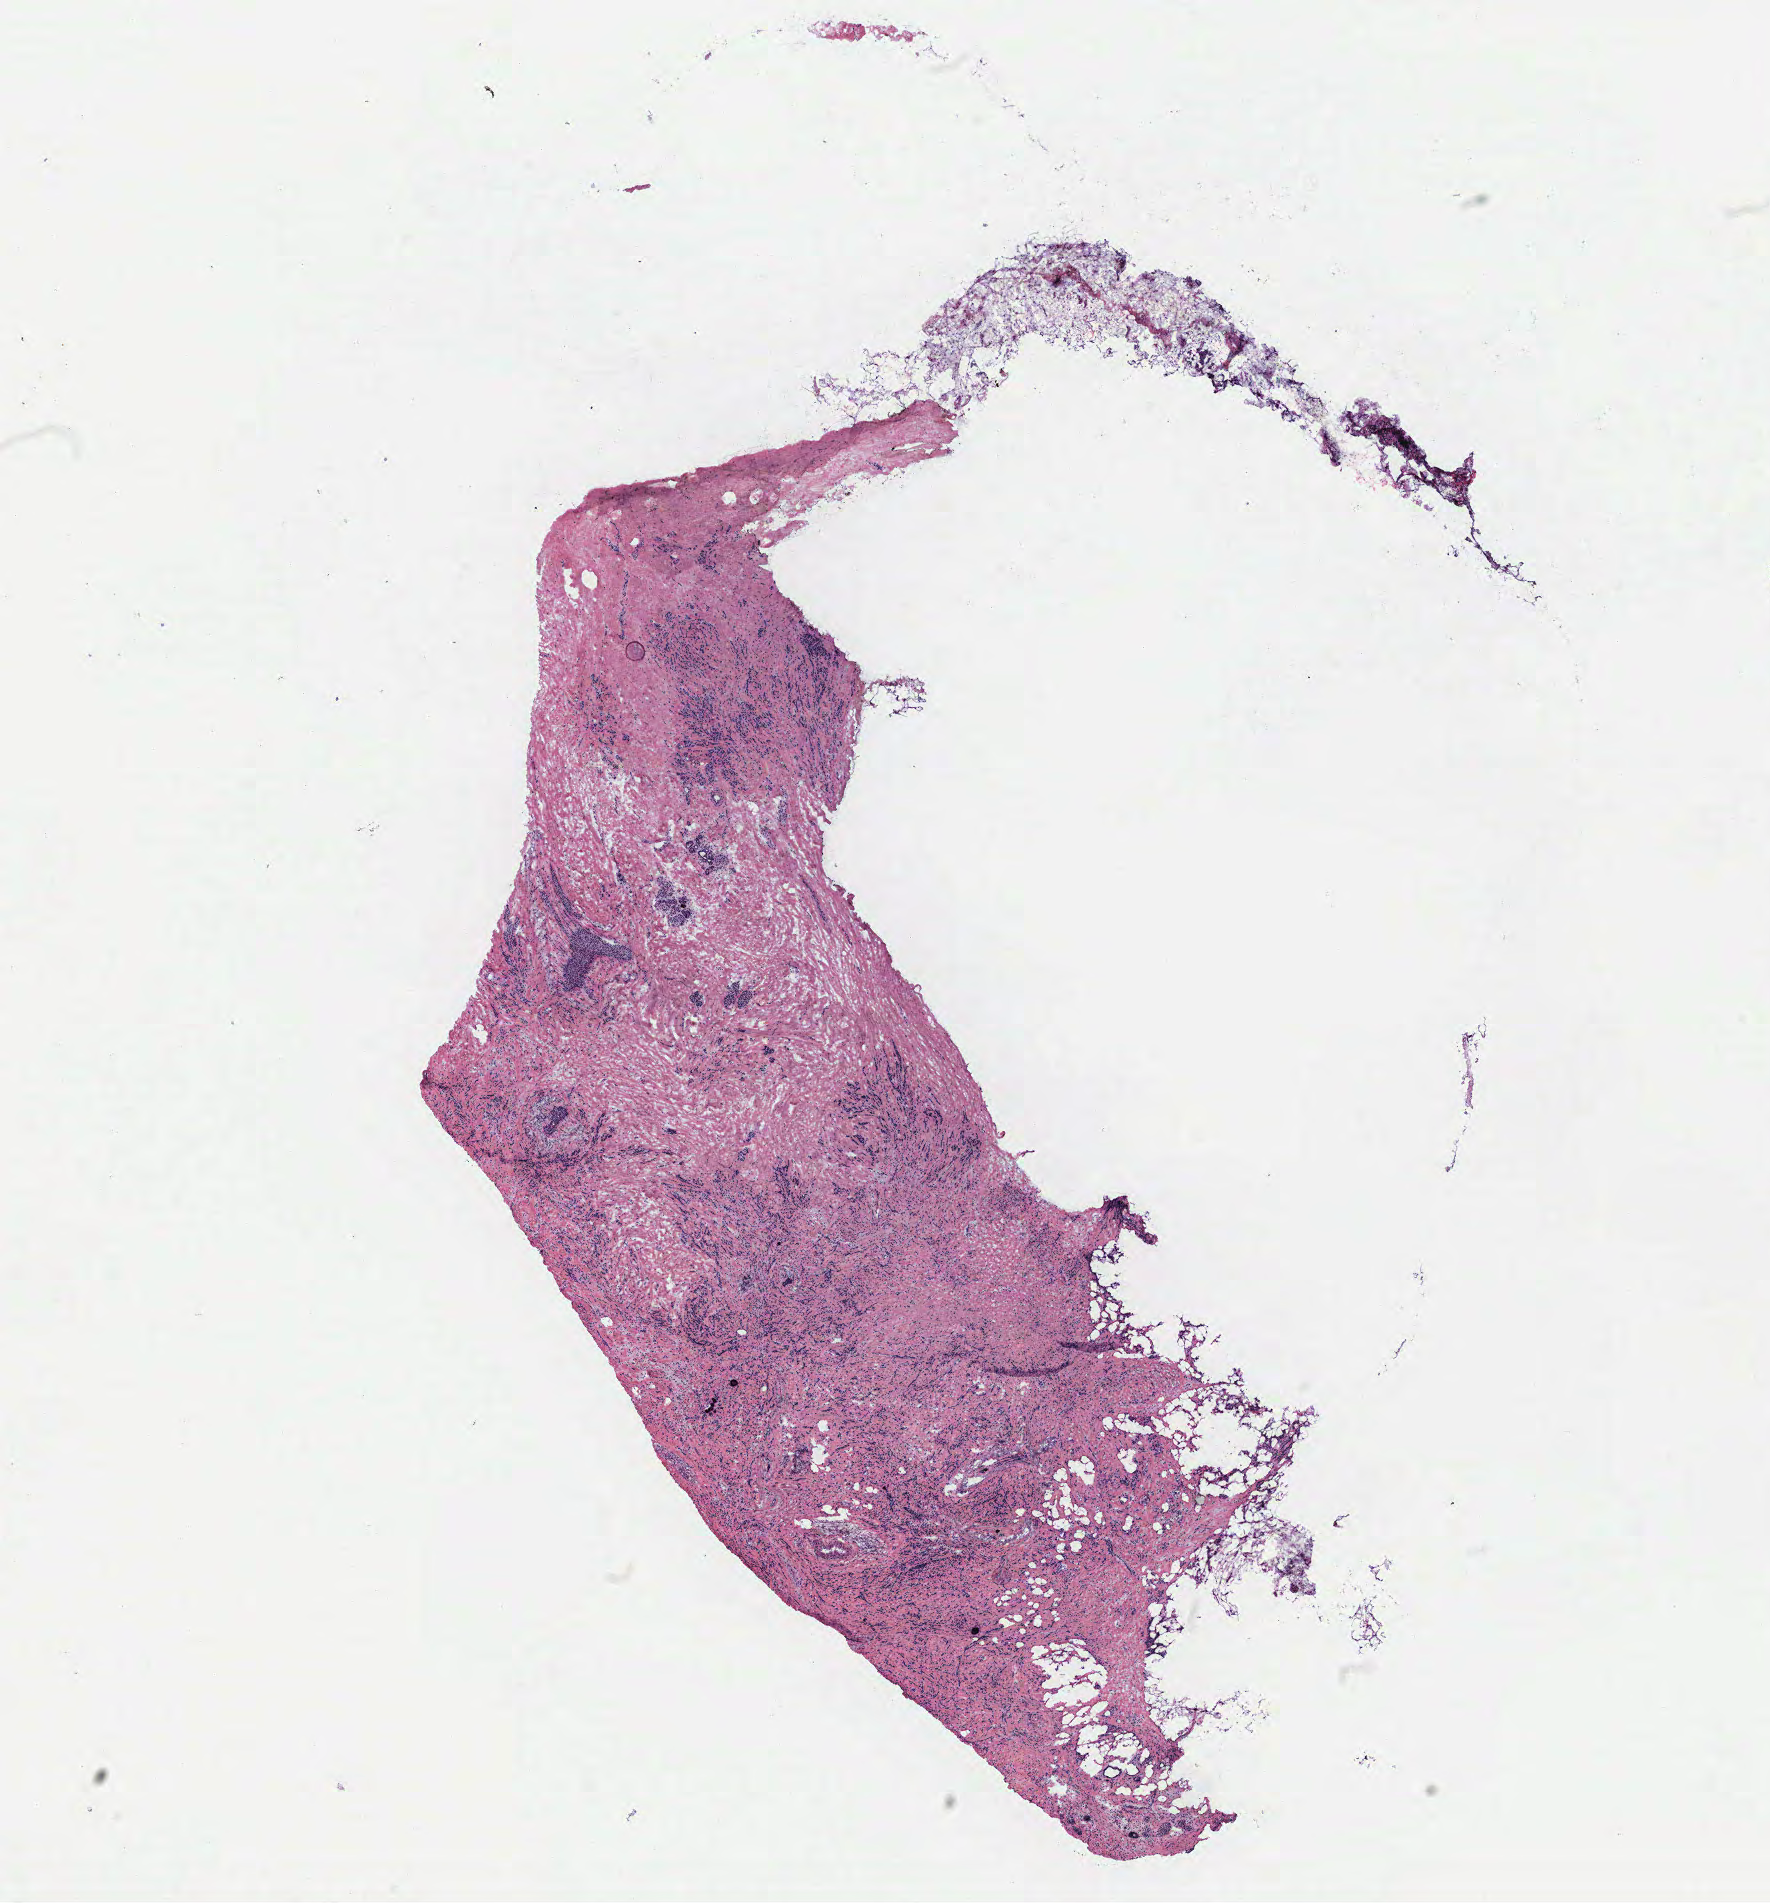
Digitized H&E tissue section (whole slide) — whole scanned area (about 14.2 x 15.2 mm, from a 40x scan) shown as a low-resolution overview; breast, tissue type not recorded. Female, 65 y/o.
Patient diagnosis: Infiltrating lobular carcinoma, NOS.